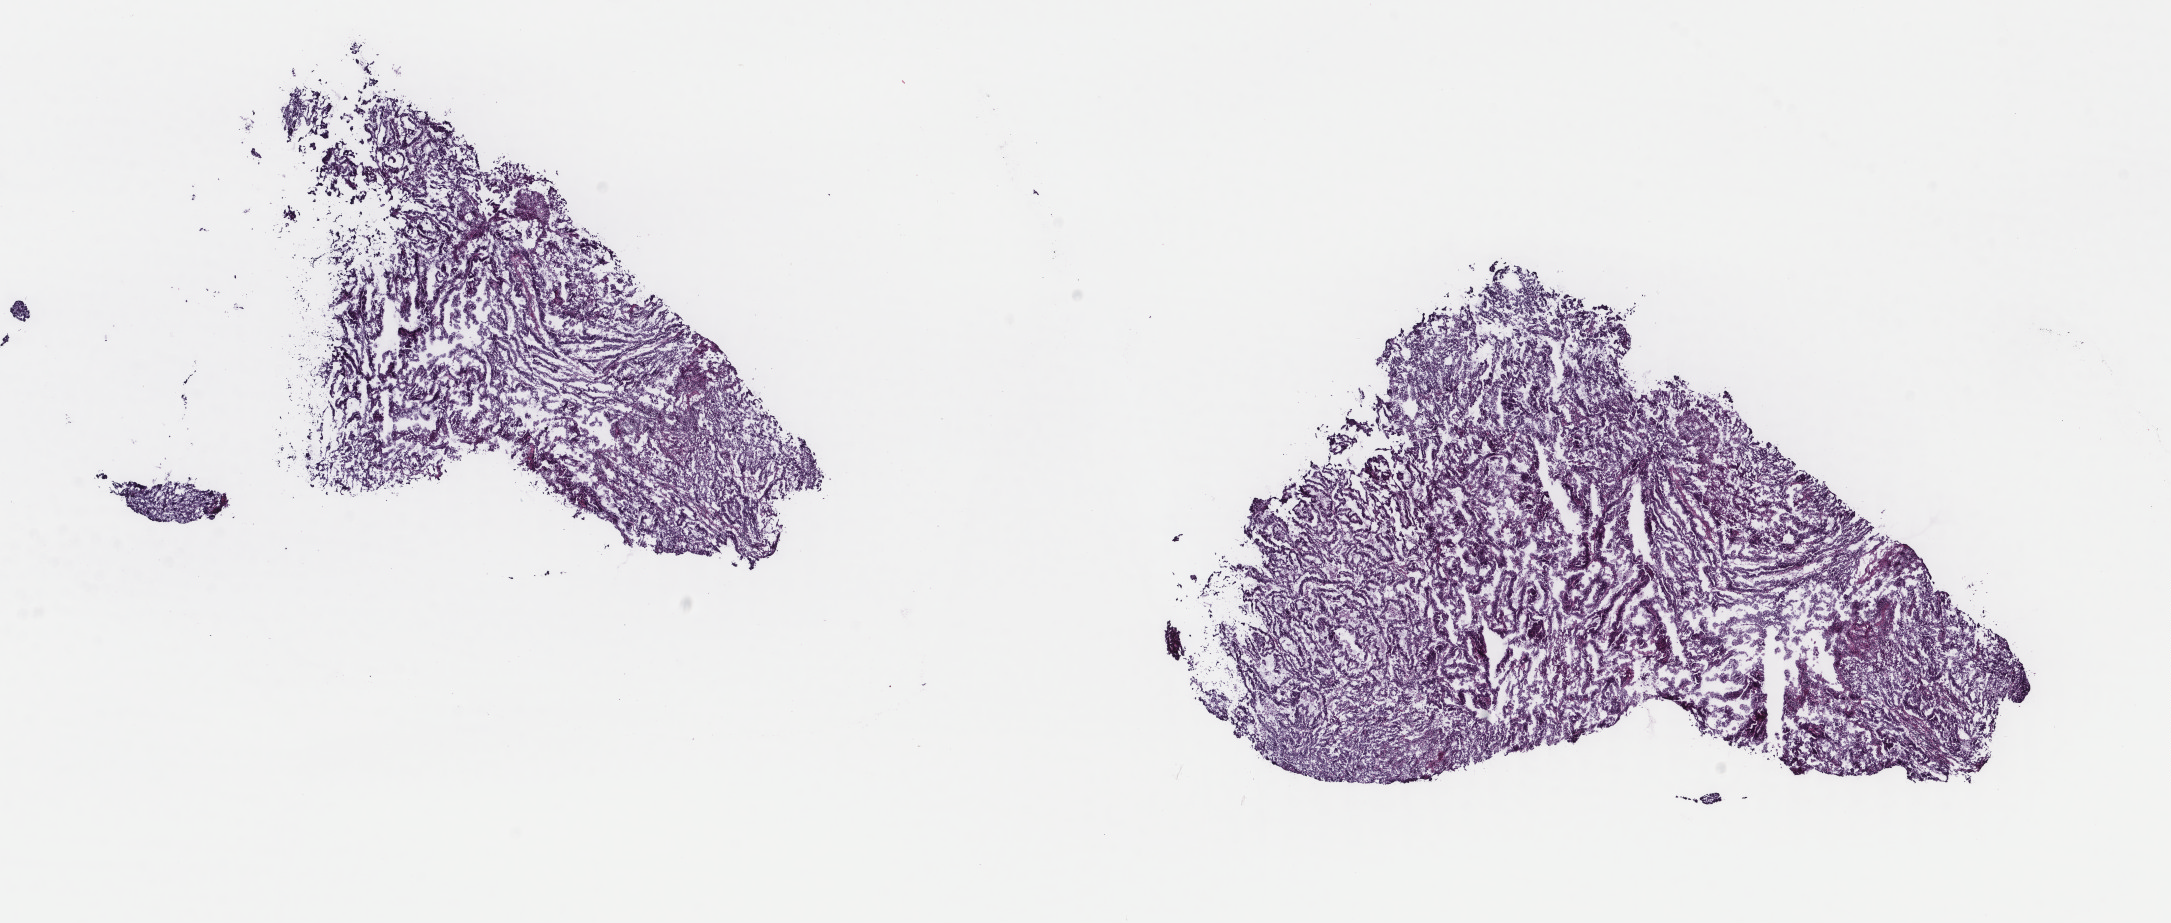
Whole-slide histology image, Hematoxylin and eosin (H&E) stained, shown as a low-resolution overview of the whole scanned area (about 17.2 x 7.3 mm), frozen section from the top of the tissue portion, sample: primary tumour, uterus. Female, age 67 years at initial diagnosis.
Pathologic diagnosis: Endometrioid adenocarcinoma, NOS (endometrium).